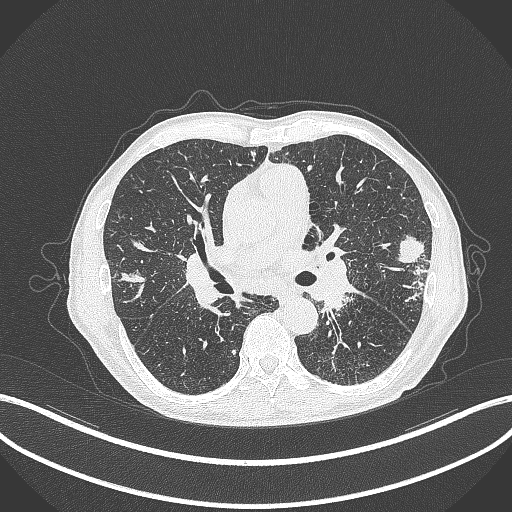
Chest CT, one axial slice. Position 223 of 463 along the scan axis. Reconstruction kernel B70f. 120 kVp. Lung window (W 1500 / L -600 HU). 1 mm slice thickness. 512 × 512 image matrix, field of view 400 × 400 mm. Male patient, age 74 years. From the clinical record (not read from this slice): clinical TNM (as recorded): T2a N1 M0.
Annotated regions visible in this slice (rectangle marked by the reading radiologist):
- lung tumour (recorded histology: adenocarcinoma): box from (x=397, y=232) to (x=430, y=268) px